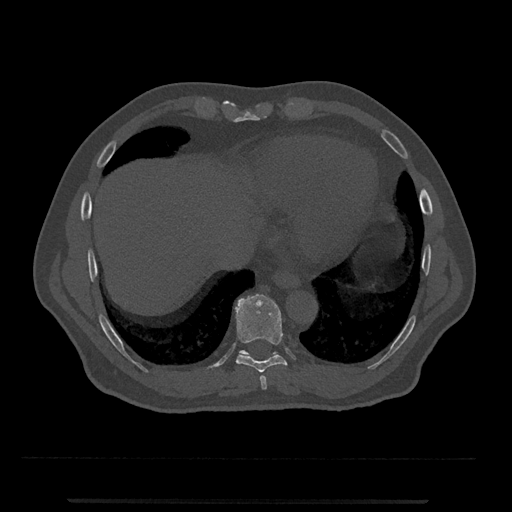
CT including the spine, one axial slice; slice 565 of 797 in the series (ordered by position); reconstruction kernel Br40s/3; 120 kVp; bone window (W 1800 / L 400 HU); 512 × 512 image matrix, field of view 419 × 419 mm. Patient: male, 63 years. From the clinical record (not read from this slice): primary cancer: prostate.
Structures marked on this image (semi-automatic segmentation, software-assisted and operator-edited):
- T10 vertebra: bounding box [x1, y1, x2, y2] px = [239, 350, 278, 356]
- T8 vertebra: [260, 375, 267, 390]
- T9 vertebra: [235, 294, 288, 372]